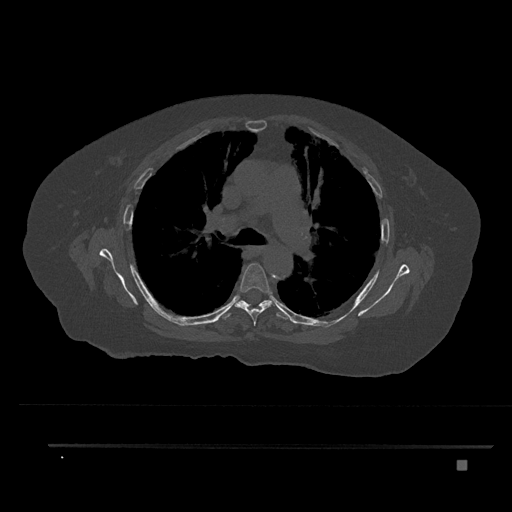
CT including the spine, one axial slice. Position 555 of 797 along the scan axis. Bone window (W 1800 / L 400 HU). 0.5 mm slice thickness. 512 × 512 image matrix. Patient: female, 76 years. From the clinical record (not read from this slice): primary cancer: lung; vertebrae with lytic lesions (as recorded): T11, L3.
Structures marked on this image (semi-automatically segmented with operator editing):
- T5 vertebra: bounding box <234,263,274,325> (left, top, right, bottom; pixels)
- T6 vertebra: <219,300,290,320>